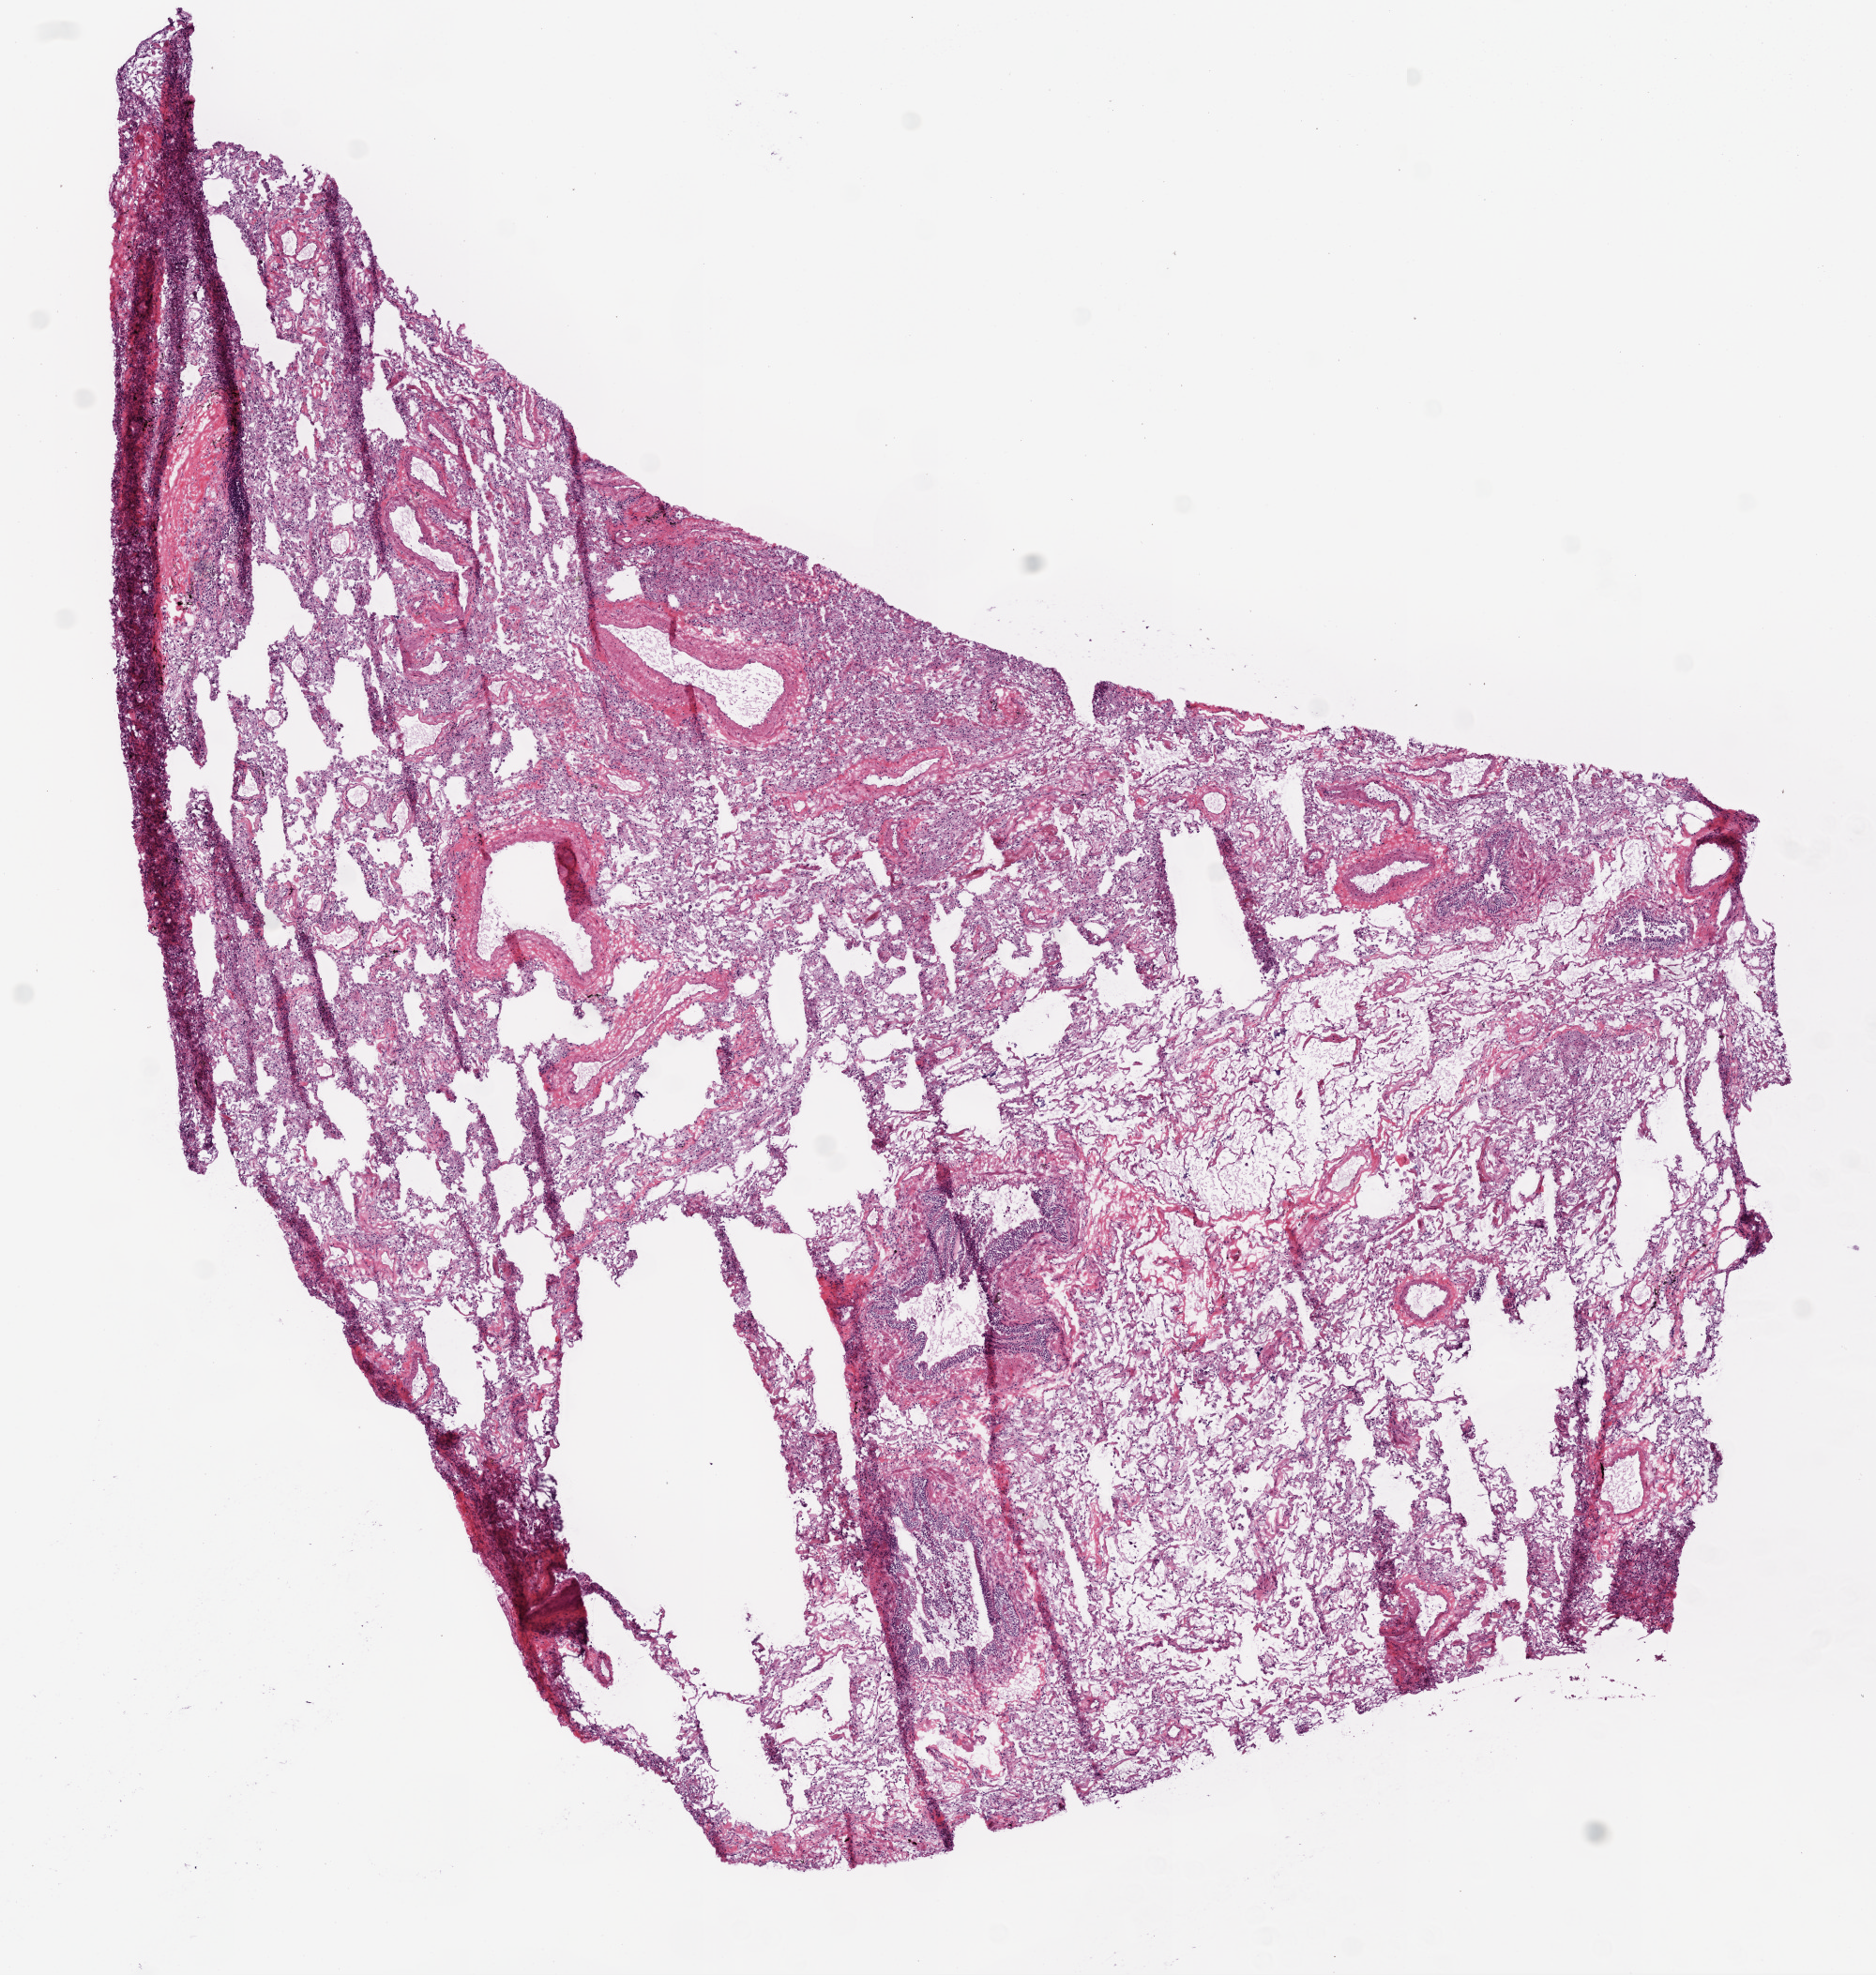
Whole-slide histology image, H&E-stained — whole scanned area (about 8.0 x 8.4 mm) shown as a low-resolution overview, frozen section, solid tissue normal (non-tumour tissue) sample from the lung. Patient: male, age at initial diagnosis 66 years.
This section: solid tissue normal (non-tumour) sample from the same patient. Patient diagnosis: Squamous cell carcinoma, NOS (upper lobe, lung).